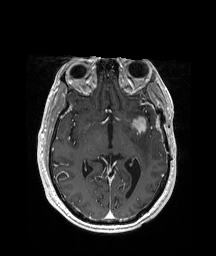
Brain MRI from a brain-tumour surgery series, one axial slice. Position 113 of 208 along the scan axis. T1-weighted post-contrast. 1 mm slice thickness. 216 × 256 image matrix. From the clinical record (not read from this slice): histopathology: Glioblastoma; WHO grade: 4; IDH mutation: no.
Annotated regions visible in this slice (outlined manually by an expert reader):
- tumour: bounding box (x1, y1, x2, y2) in pixels: (123, 116, 158, 132)